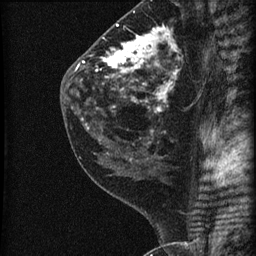
Breast MRI (dynamic contrast-enhanced), one sagittal slice; slice 29 of 60 in the series (ordered by position); dynamic contrast-enhanced series, image 2 of 3 at this slice position (ordered by acquisition); 1.5 T; TE 4.2 ms, TR 22.7 ms; 1.8 mm slice thickness; 256 × 256 image matrix, field of view 180 × 180 mm. Female patient, age 45 years. From the clinical record (not read from this slice): setting: breast cancer imaged before/during neoadjuvant chemotherapy; receptor status: HR-positive, HER2-negative.
Structures marked on this image (semi-automatic segmentation, software-assisted and operator-edited):
- analysis volume of interest (the breast-tissue region the enhancement analysis was run in; not a lesion): bounding box [x1, y1, x2, y2] px = [74, 11, 205, 140]
- tumour enhancement mask (voxels above the 90 % enhancement threshold inside the analysis volume of interest): [75, 25, 178, 111]